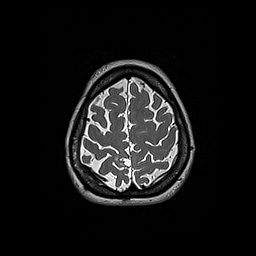
Brain MRI from a brain-tumour surgery series, one axial slice; position 47 of 192 along the scan axis; 1 mm slice thickness; 256 × 256 image matrix, field of view 250 × 250 mm. Case-level facts recorded for this patient, not image findings: histopathology: Oligodendroglioma; WHO grade: 2; IDH mutation: yes.
Annotated regions visible in this slice (outlined manually by an expert reader):
- tumour: bounding box <115,156,118,161> (left, top, right, bottom; pixels)